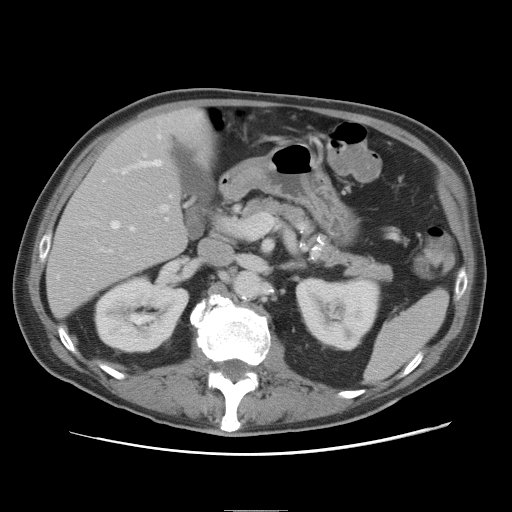
Contrast-enhanced abdominal CT, one axial slice; position 37 of 89 along the scan axis; 120 kVp; intravenous contrast given; soft-tissue window (W 400 / L 40 HU); 5 mm slice thickness; 512 × 512 image matrix, field of view 375 × 375 mm. Male patient, age 69 years. Case-level facts recorded for this patient, not image findings: diagnosis: colorectal cancer liver metastases, imaged before liver resection; multiple liver metastases: no; largest metastasis: 8.5 cm; chemotherapy before resection: no.
Annotated regions visible in this slice (expert manual segmentation):
- hepatic veins: bounding box <112,135,172,230> (left, top, right, bottom; pixels)
- liver: <47,109,213,315>
- planned liver remnant (the part of the liver to remain after resection): <47,109,212,316>
- portal vein (with intrahepatic branches): <109,204,170,252>